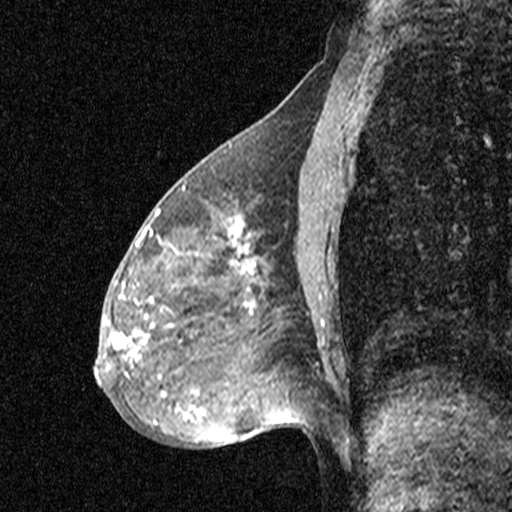
Breast MRI (dynamic contrast-enhanced), one sagittal slice. Position 22 of 44 along the scan axis. Dynamic contrast-enhanced study with each time point stored as its own series, time point 2 of 3 at this slice position (early post-contrast, ordered by acquisition time). 1.5 T. TE 4.5 ms, TR 11 ms. 3 mm slice thickness. 512 × 512 image matrix. Female patient, age 53 years. From the clinical record (not read from this slice): setting: breast cancer imaged before/during neoadjuvant chemotherapy; receptor status: HR-positive, HER2-negative.
Outlined on this slice (semi-automatically segmented with operator editing):
- analysis volume of interest (the breast-tissue region the enhancement analysis was run in; not a lesion): bounding box [x1, y1, x2, y2] px = [88, 176, 313, 423]
- tumour enhancement mask (voxels above the 90 % enhancement threshold inside the analysis volume of interest): [95, 210, 254, 418]